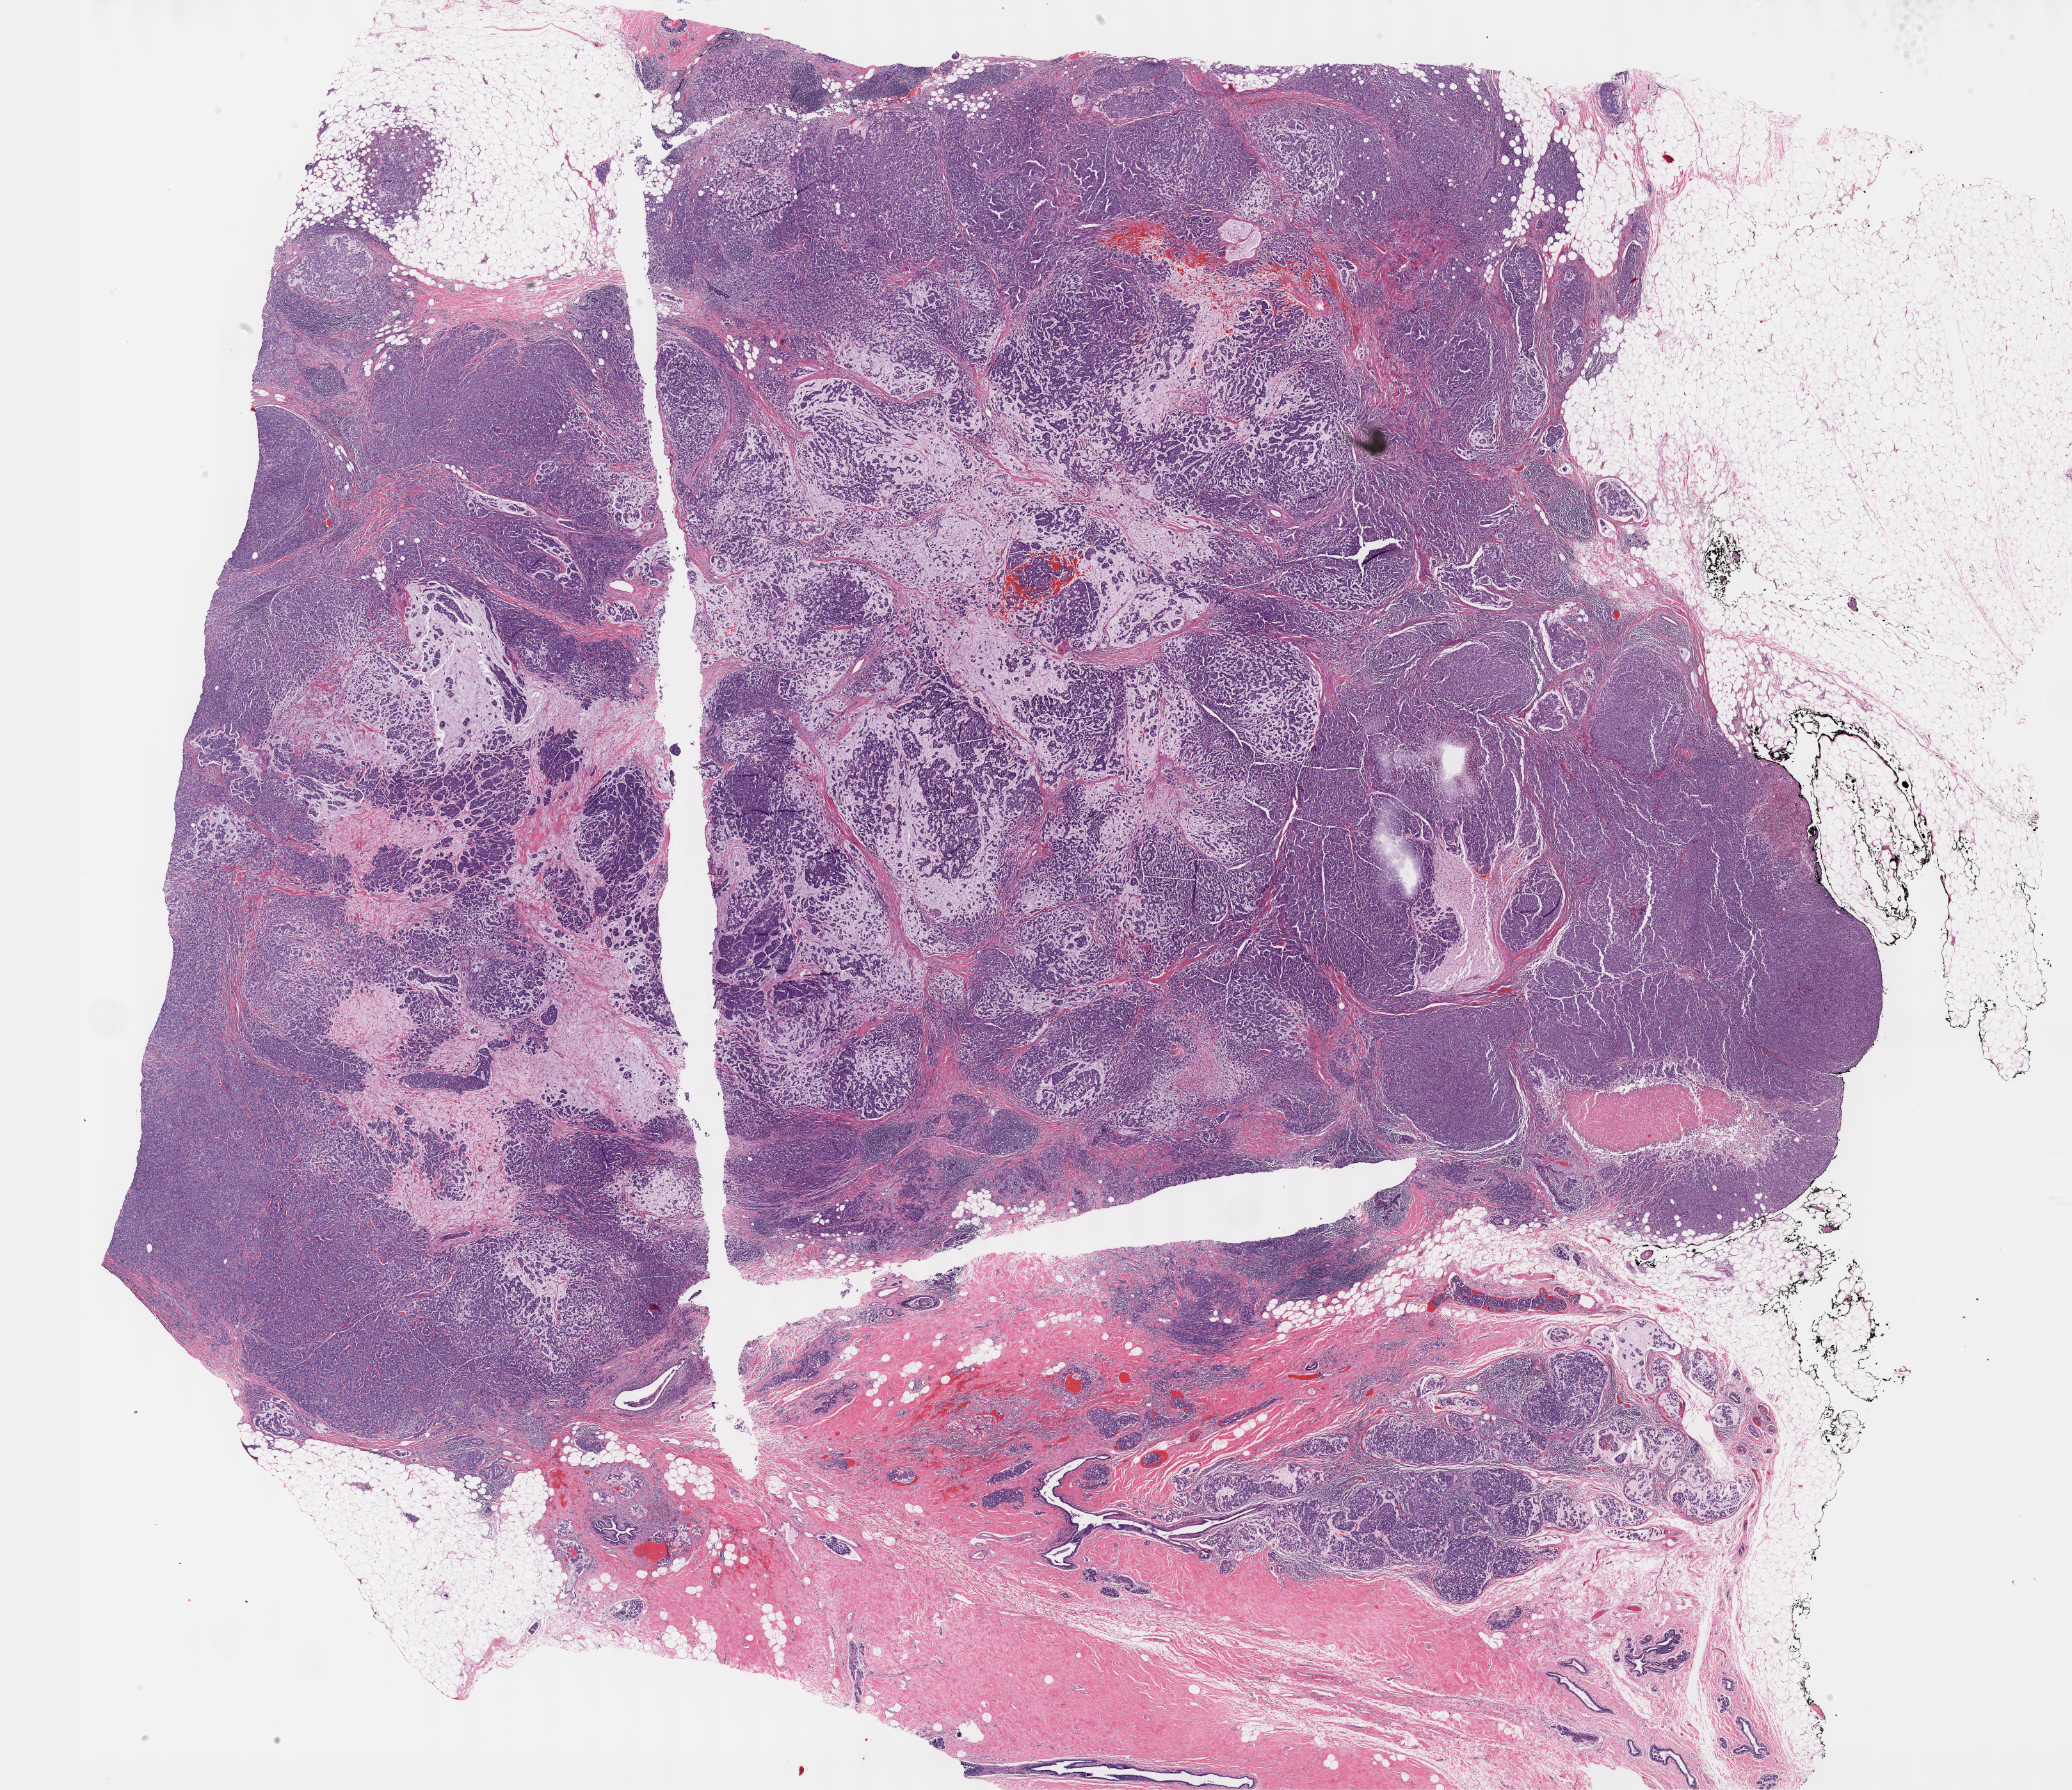
Whole-slide histology image, H&E, low-resolution overview of the scanned area, about 26.2 x 22.6 mm (from a 40x scan), formalin-fixed paraffin-embedded (FFPE) diagnostic section, primary tumour sample from the breast. Patient: female, age at initial diagnosis 52 years.
Pathologic diagnosis: Infiltrating duct mixed with other types of carcinoma.